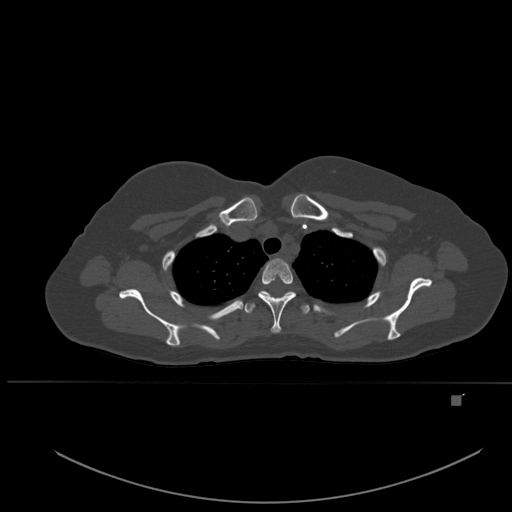
CT including the spine, one axial slice. Slice 403 of 651 in the series (ordered by position). Bone window (W 1800 / L 400 HU). 1.5 mm slice thickness. 512 × 512 image matrix, field of view 443 × 443 mm. Female patient, age 49 years. From the clinical record (not read from this slice): primary cancer: breast; vertebrae with lytic lesions (as recorded): L3, T12, L4.
Annotated regions visible in this slice (semi-automatically segmented with operator editing):
- T2 vertebra: bounding box <258,258,296,333> (left, top, right, bottom; pixels)
- T3 vertebra: <244,291,310,314>